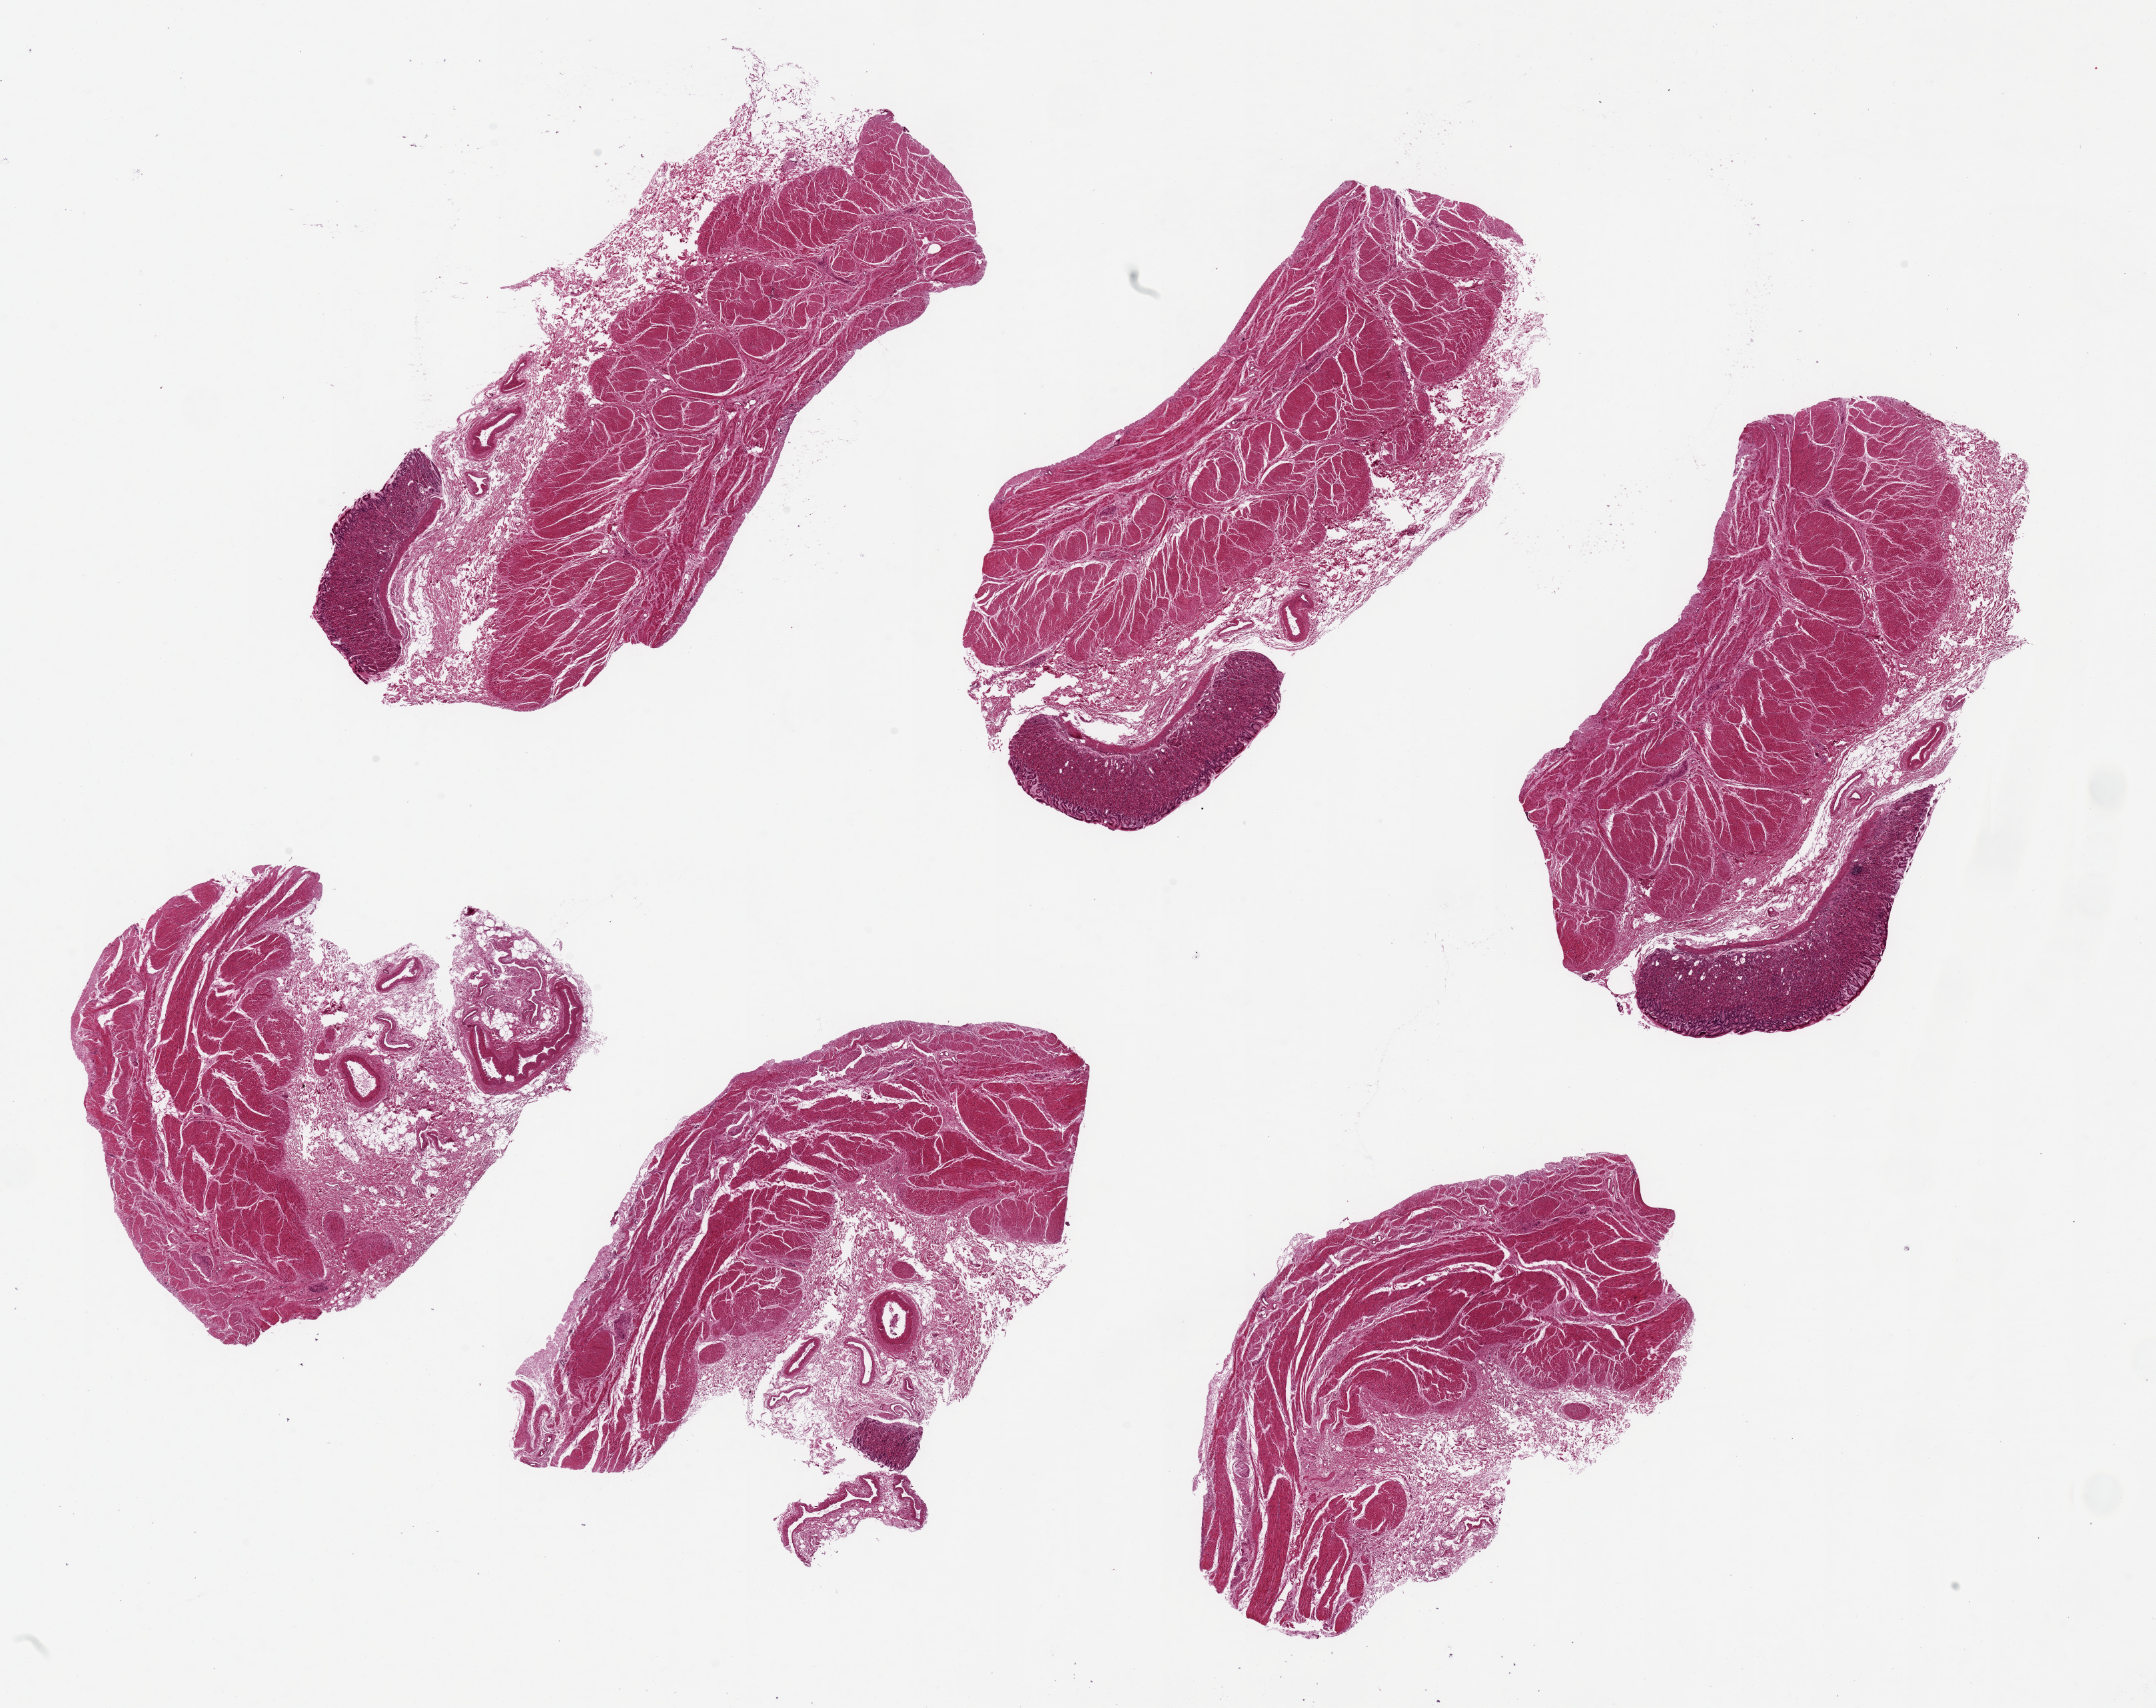
Digitized hematoxylin and eosin (H&E)-stained section, brightfield — a low-resolution overview of the entire scanned area, about 25.6 x 20.3 mm. PAXgene-fixed, paraffin-embedded tissue. Sampled site (target tissue): stomach. Donor tissue sample. Male donor.
* pathologist's review note for this sample: 6 pieces ~8x3mm. Mucosa well-presereved but only focally present in 4 aliquots, where prsent ~20% of thickness